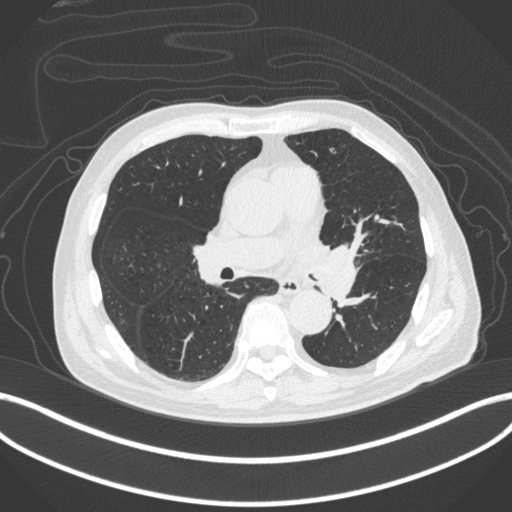
Chest CT, one axial slice. Slice 232 of 420 in the series (ordered by position). Reconstruction kernel B31f. 120 kVp. Lung window (W 1500 / L -600 HU). 1 mm slice thickness. 512 × 512 image matrix. Patient: male, 77 years. From the clinical record (not read from this slice): clinical TNM (as recorded): T3 N1 M0.
Outlined on this slice (bounding box drawn by a radiologist):
- lung tumour (recorded histology: adenocarcinoma): bounding box [x1, y1, x2, y2] px = [304, 240, 362, 308]